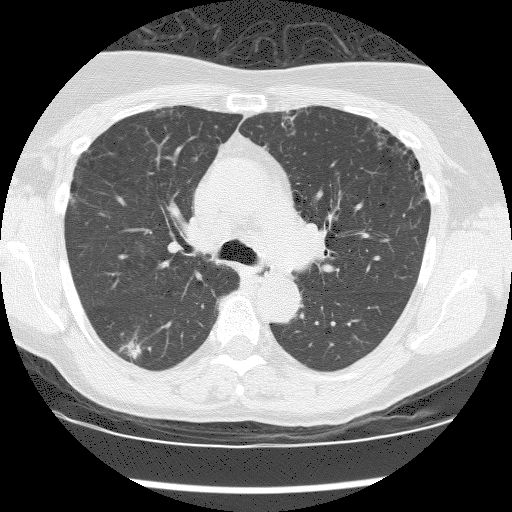
Low-dose screening chest CT, one axial slice; slice 121 of 176 in the series (ordered by position); reconstruction kernel BONE; 120 kVp; lung window (W 1500 / L -600 HU); 2.5 mm slice thickness; 512 × 512 image matrix, field of view 320 × 320 mm.
Outlined on this slice (expert manual segmentation):
- lesion 1 (tumor, lower lobe of right lung): bounding box (x1, y1, x2, y2) in pixels: (125, 340, 141, 359)